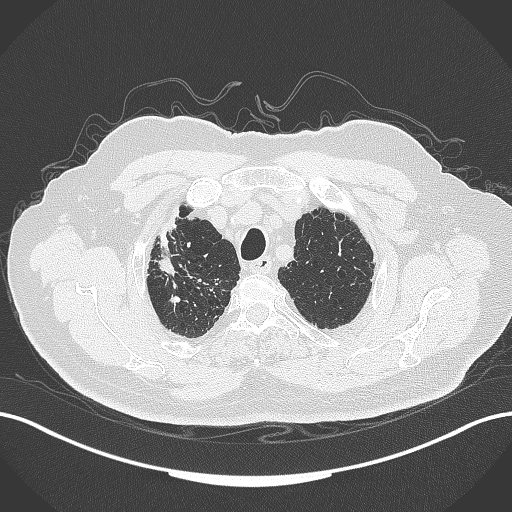
Chest CT, one axial slice. Position 305 of 389 along the scan axis. Reconstruction kernel B70f. Lung window (W 1500 / L -600 HU). 1 mm slice thickness. 512 × 512 image matrix, field of view 400 × 400 mm. Male patient, age 72 years. From the clinical record (not read from this slice): clinical TNM (as recorded): T1a N0 M0.
Structures marked on this image (rectangle marked by the reading radiologist):
- lung tumour (recorded histology: squamous cell carcinoma): bounding box (x1, y1, x2, y2) in pixels: (158, 214, 183, 278)